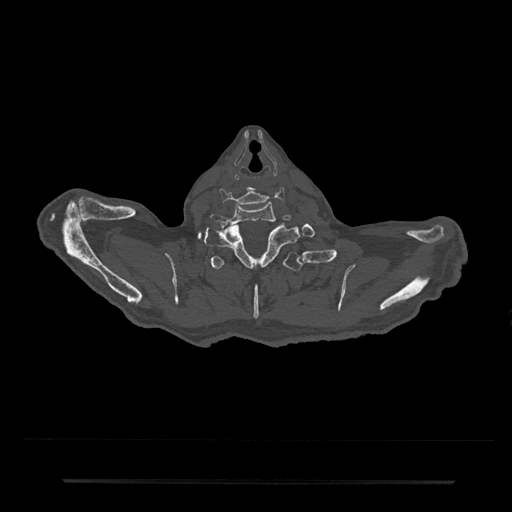
CT including the spine, one axial slice. Position 721 of 797 along the scan axis. Reconstruction kernel Br40s/3. 120 kVp. Bone window (W 1800 / L 400 HU). 512 × 512 image matrix, field of view 427 × 427 mm. Male patient, age 74 years. From the clinical record (not read from this slice): primary cancer: prostate.
Outlined on this slice (semi-automatically segmented with operator editing):
- T1 vertebra: bounding box (x1, y1, x2, y2) in pixels: (203, 221, 300, 268)
- T2 vertebra: (205, 251, 314, 319)